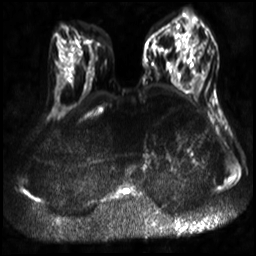
Breast MRI, one axial slice. Position 12 of 30 along the scan axis. Diffusion-weighted series; image 2 of 4 stored at this slice position (different b-values; order by instance number). 3 T. 256 × 256 image matrix. Female patient.
Outlined on this slice (manually delineated by an expert):
- tumour on diffusion-weighted imaging: bounding box [x1, y1, x2, y2] px = [193, 31, 200, 44]